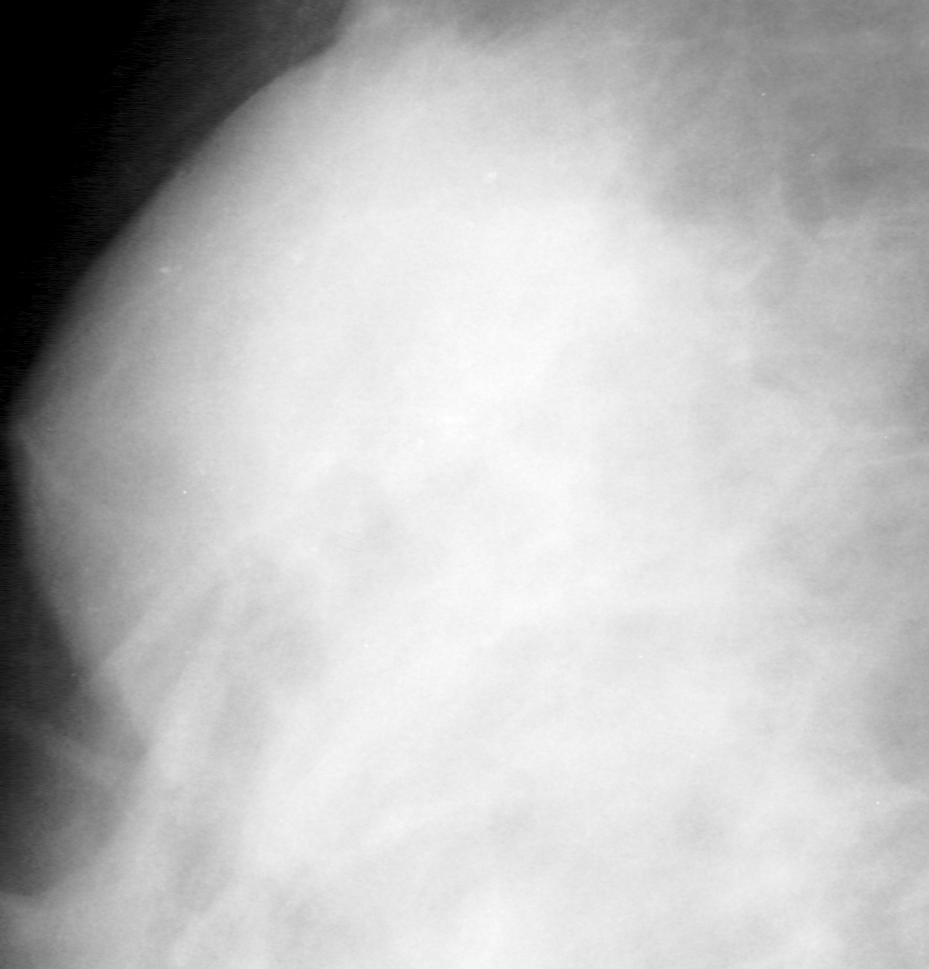
Cropped region of a digitized screen-film mammogram centred on a radiologist-marked abnormality; left breast; MLO view; BI-RADS breast density category 4 (scale 1–4).
Calcifications, morphology pleomorphic, distribution segmental; BI-RADS assessment category 4; pathology result (as recorded, not read from the image): benign.